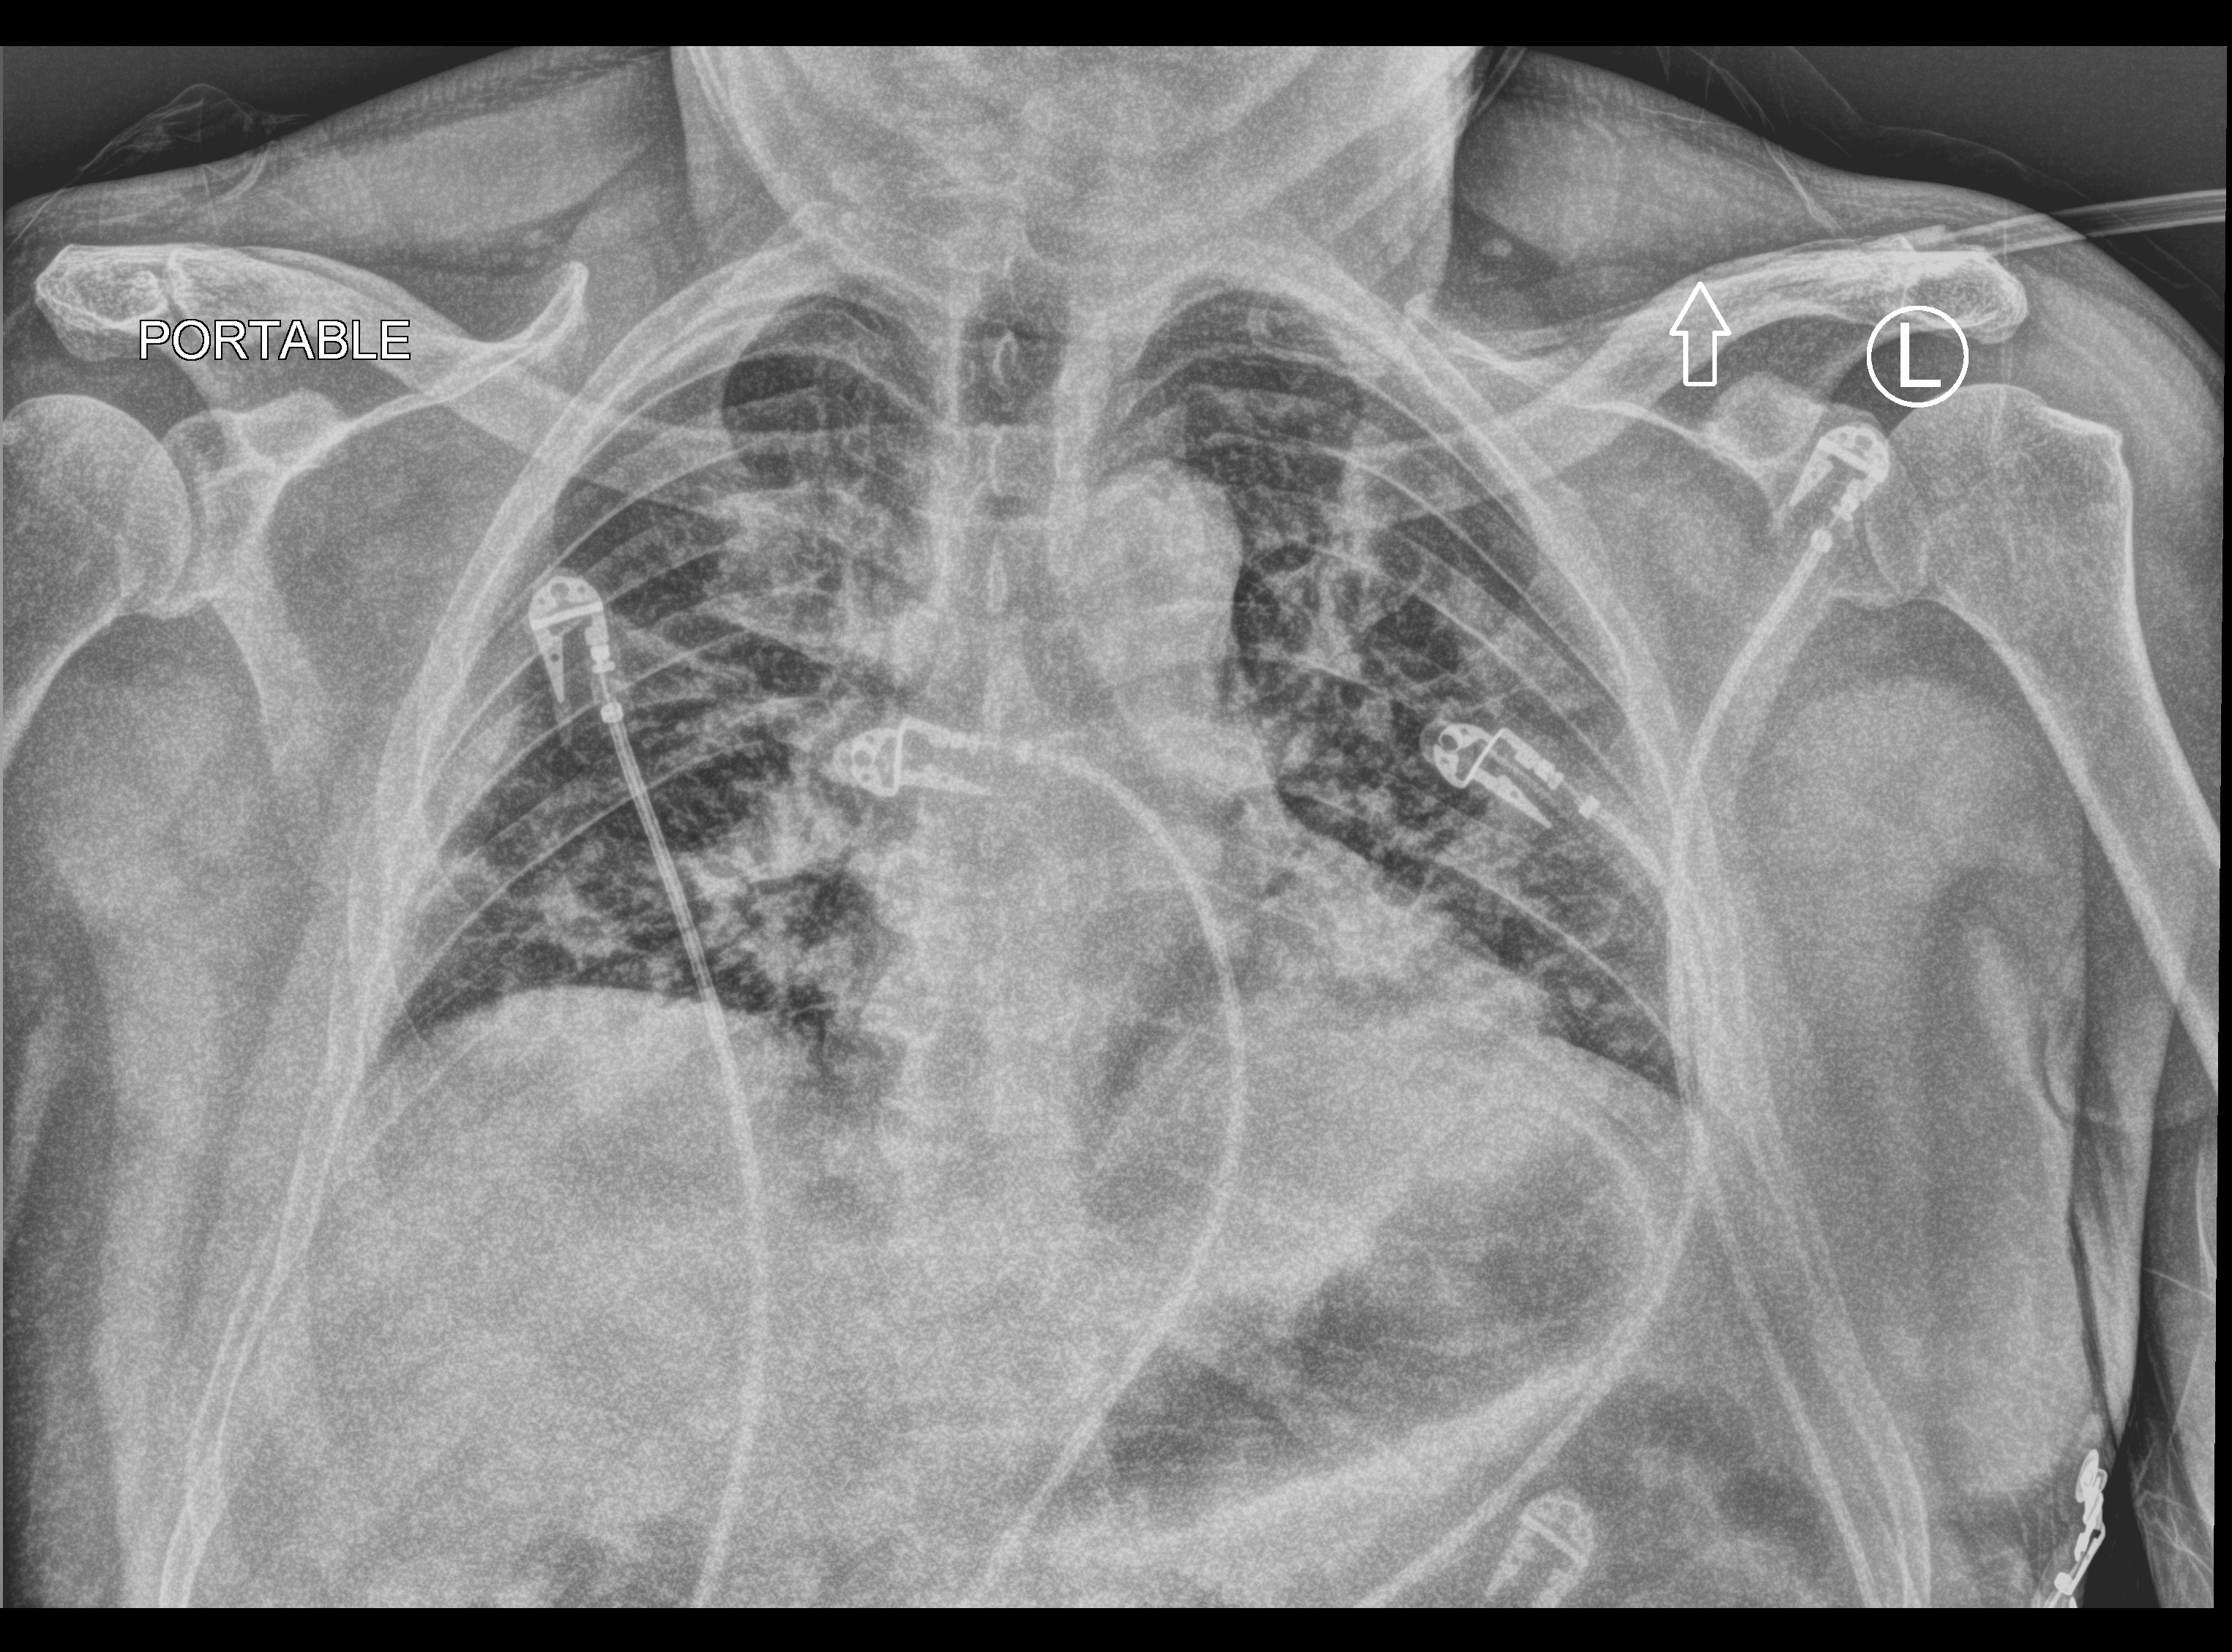
Portable chest radiograph. Patient hospitalised with COVID-19; male, aged 60–74 years.
Admission-level facts for this patient (not findings on this image; timing relative to this image not recorded): hypertension (admission record): no; admitted to intensive care during this hospital stay: no.